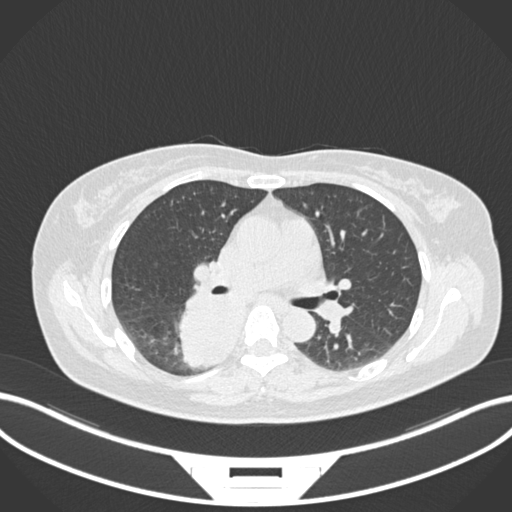
Chest CT, one axial slice. Position 606 of 677 along the scan axis. Reconstruction kernel B30f. 120 kVp. Lung window (W 1500 / L -600 HU). 512 × 512 image matrix. Patient: female, 54 years. From the clinical record (not read from this slice): clinical TNM (as recorded): T4 N0 M0.
Annotated regions visible in this slice (rectangle marked by the reading radiologist):
- lung tumour (recorded histology: adenocarcinoma): bounding box <172,284,249,372> (left, top, right, bottom; pixels)